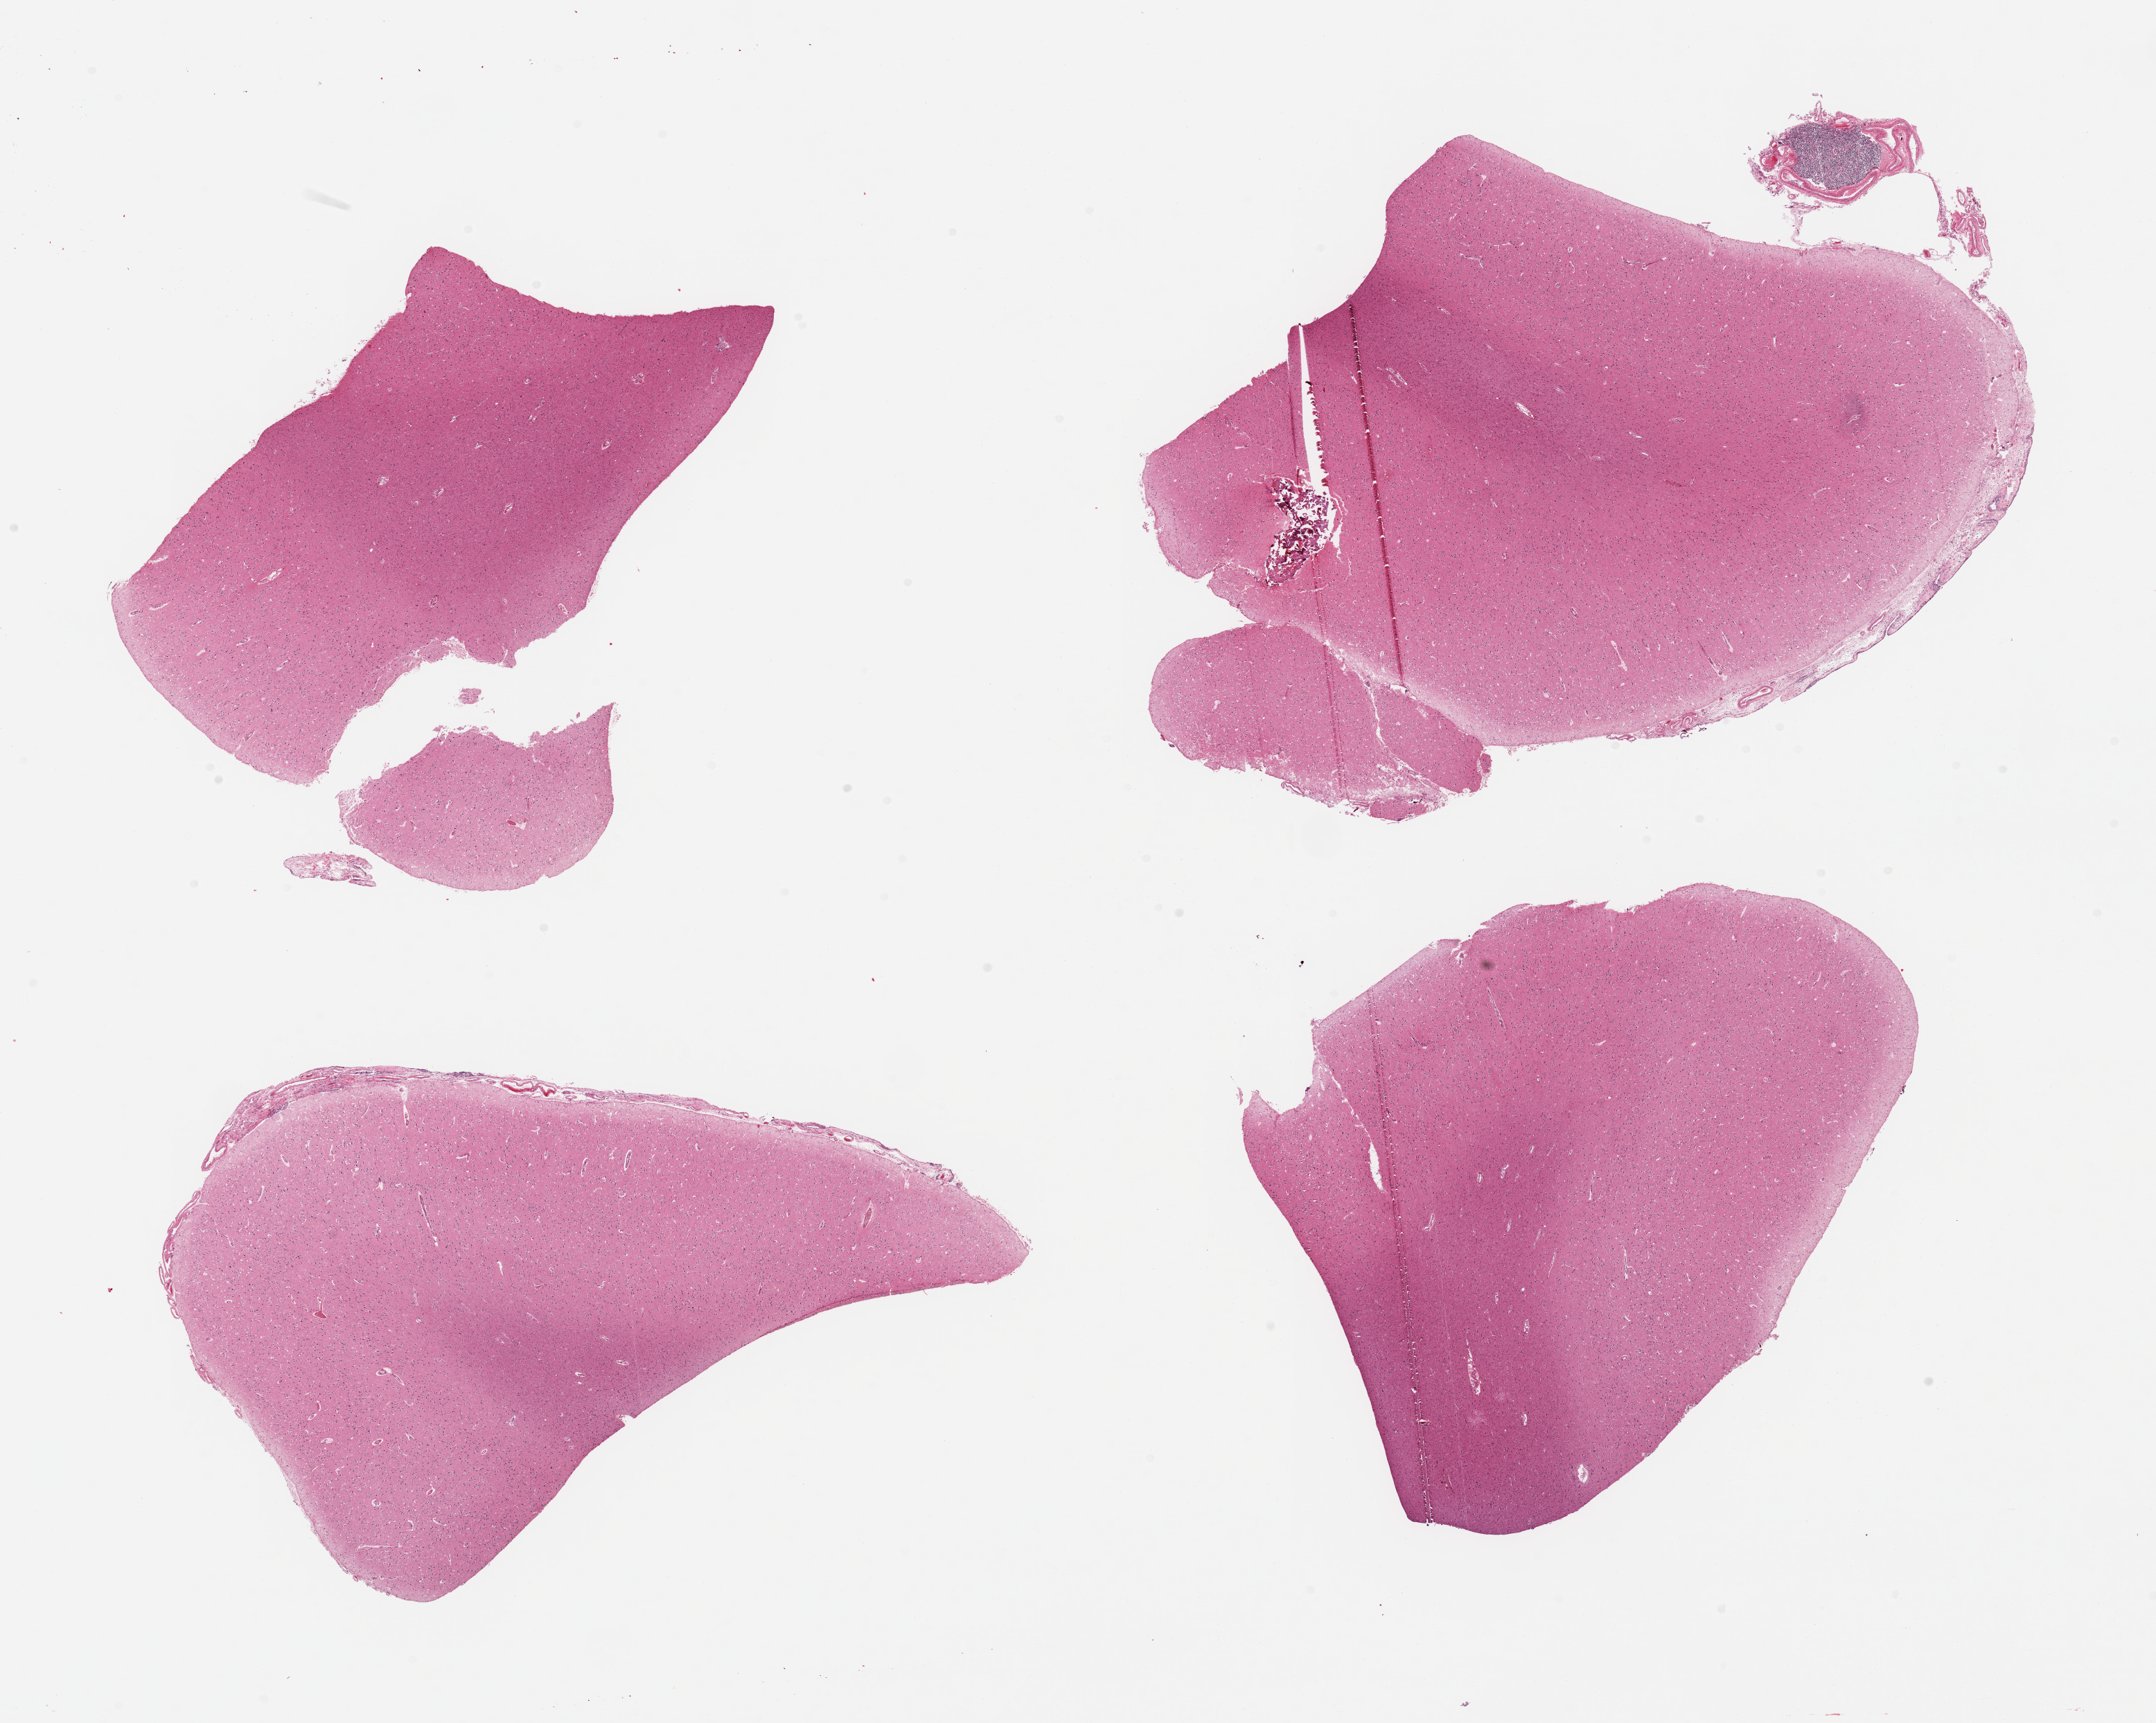
Whole-slide image, H&E stain, brightfield, whole scanned area (about 24.6 x 19.7 mm) shown as a low-resolution overview; PAXgene-fixed, paraffin-embedded tissue; section of cerebral cortex (target tissue); tissue donor sample. Male donor.
• review note (as recorded): 4 pieces; meningeal coverage noted in 2 of 4 pieces; portion of cerebellum